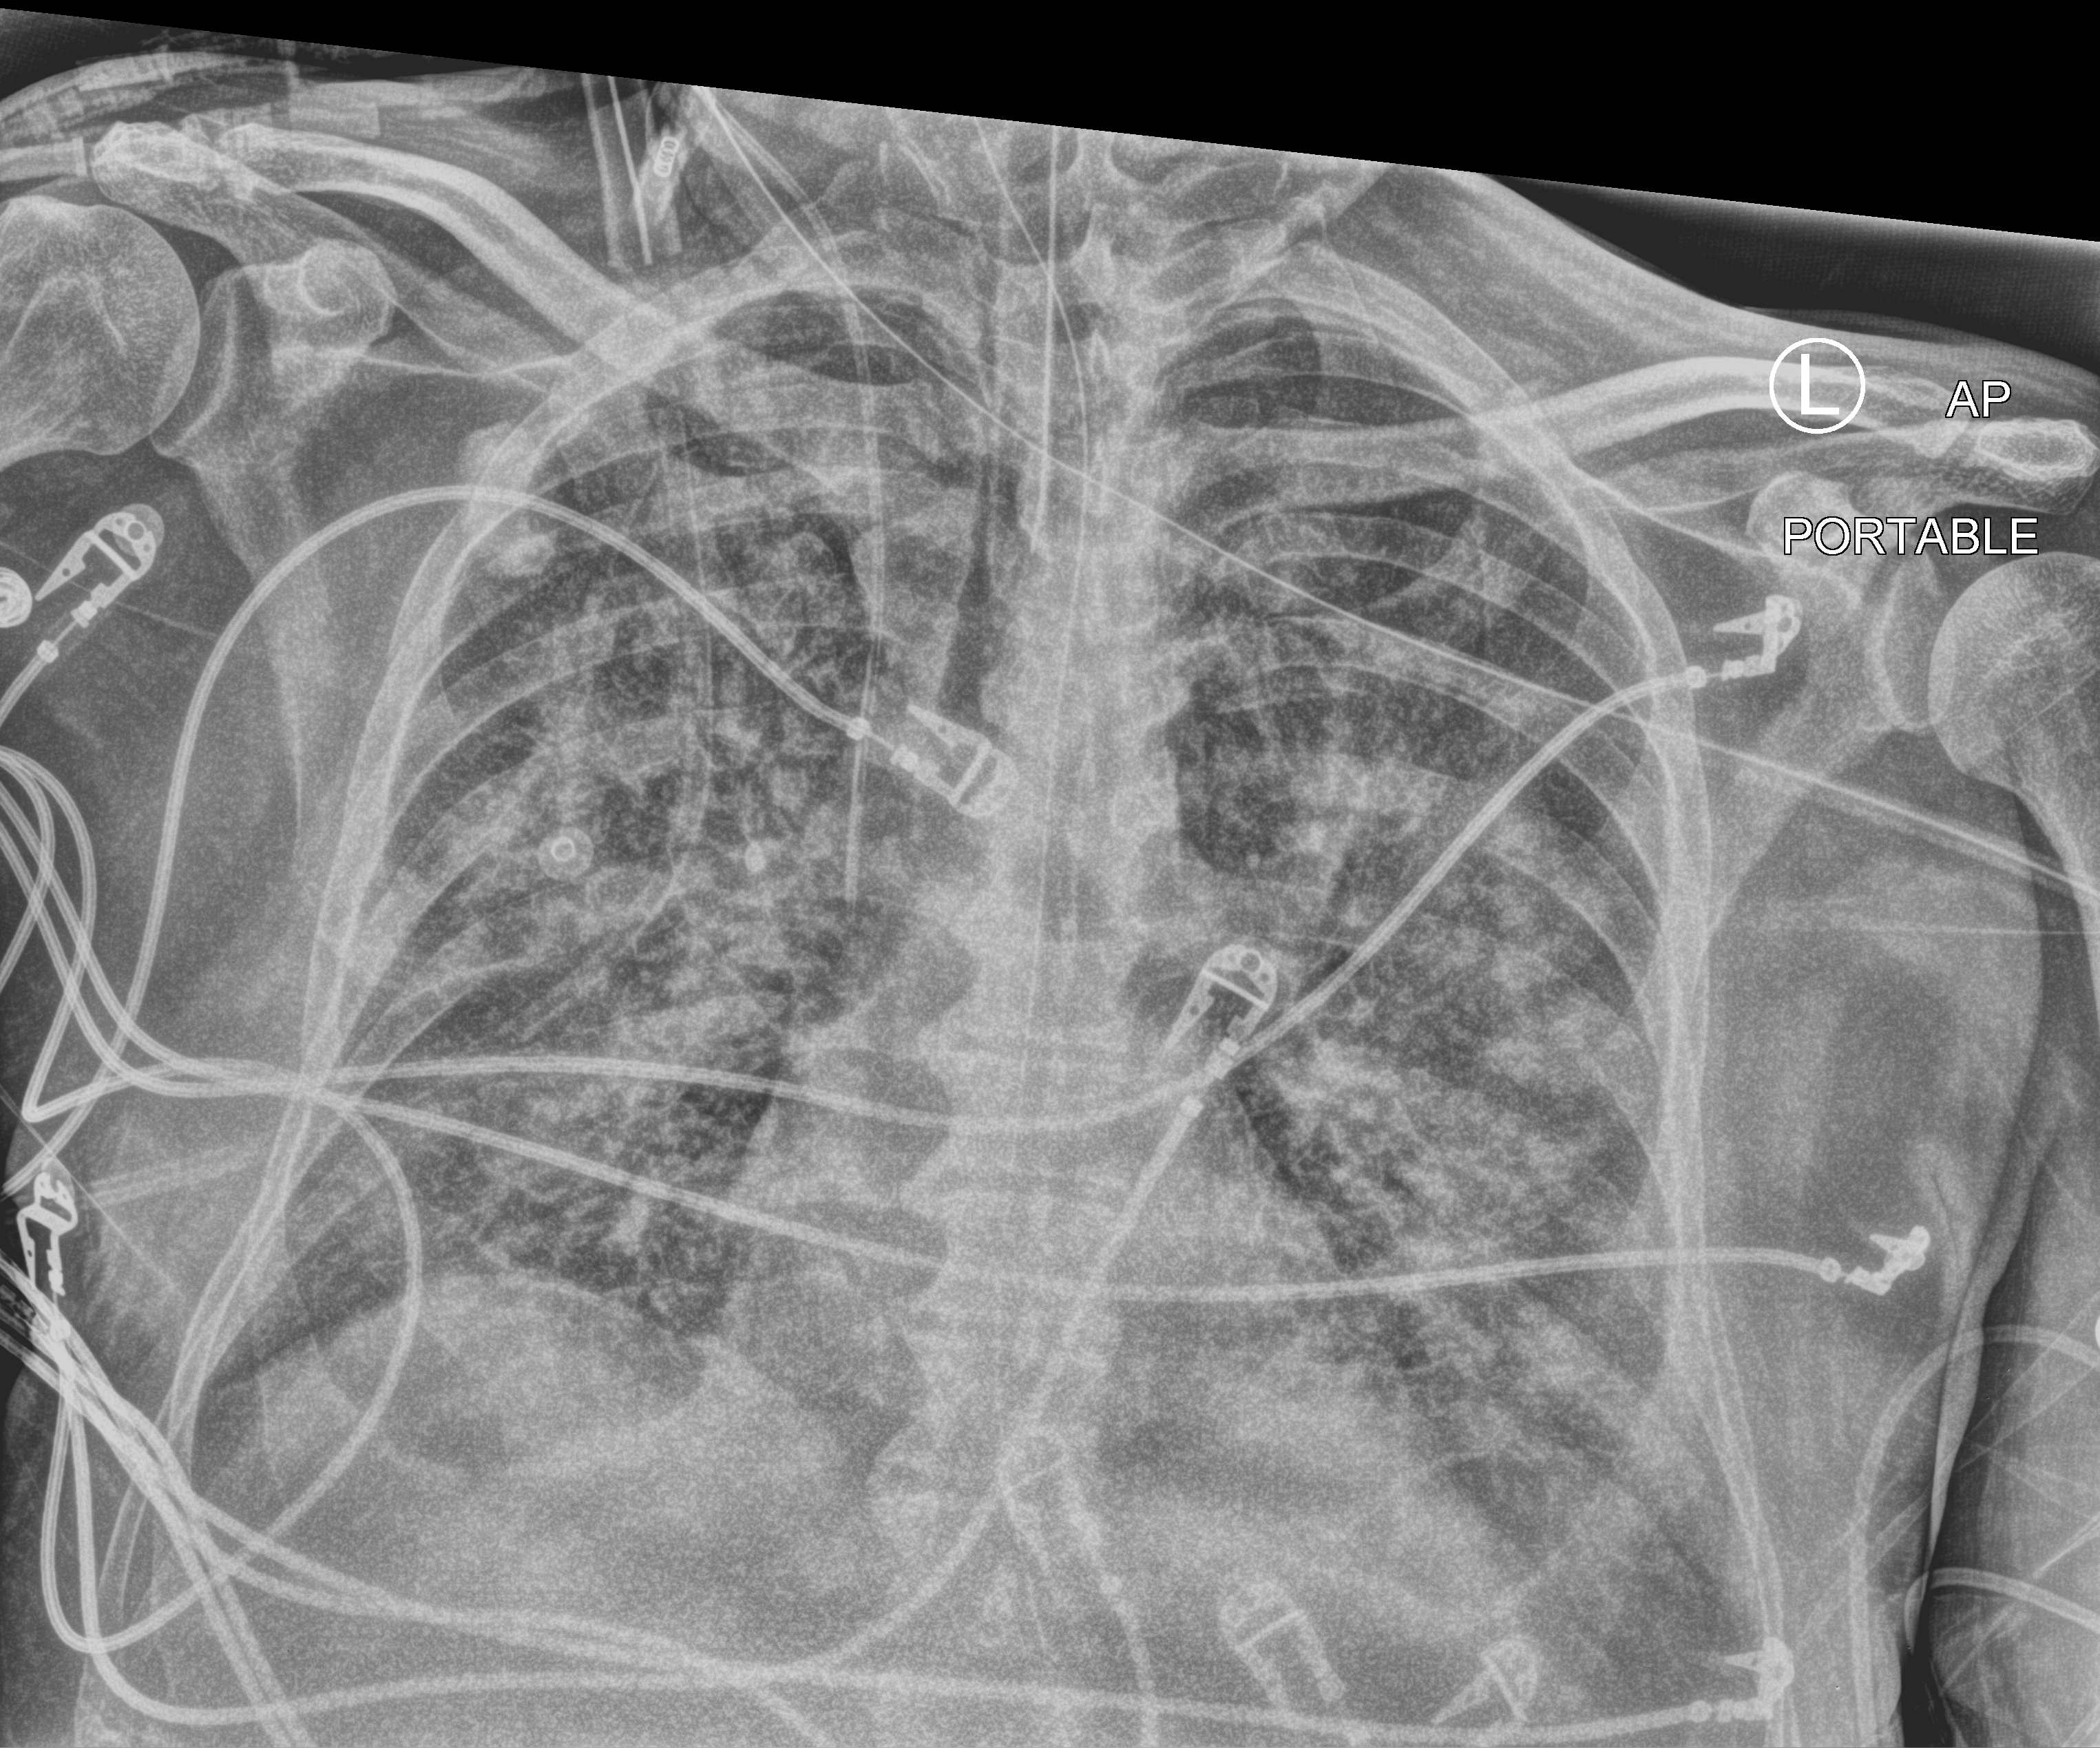
Bedside chest radiograph (computed radiography); anteroposterior (AP) projection. Patient hospitalised with COVID-19; male, aged 60–74 years.
From the hospital-stay record, not from the radiograph (when in the stay this image was taken is not recorded):
- admitted to intensive care during this hospital stay: yes